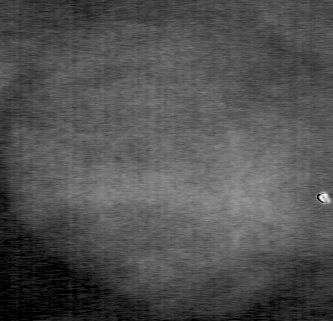
Crop from a digitized film mammogram around one marked abnormality; left breast; CC view.
Marked abnormality: mass, shape oval, margins circumscribed; BI-RADS assessment category 3; subtlety rating 3 on a 1 (subtle) to 5 (obvious) scale; pathology (as recorded): benign.